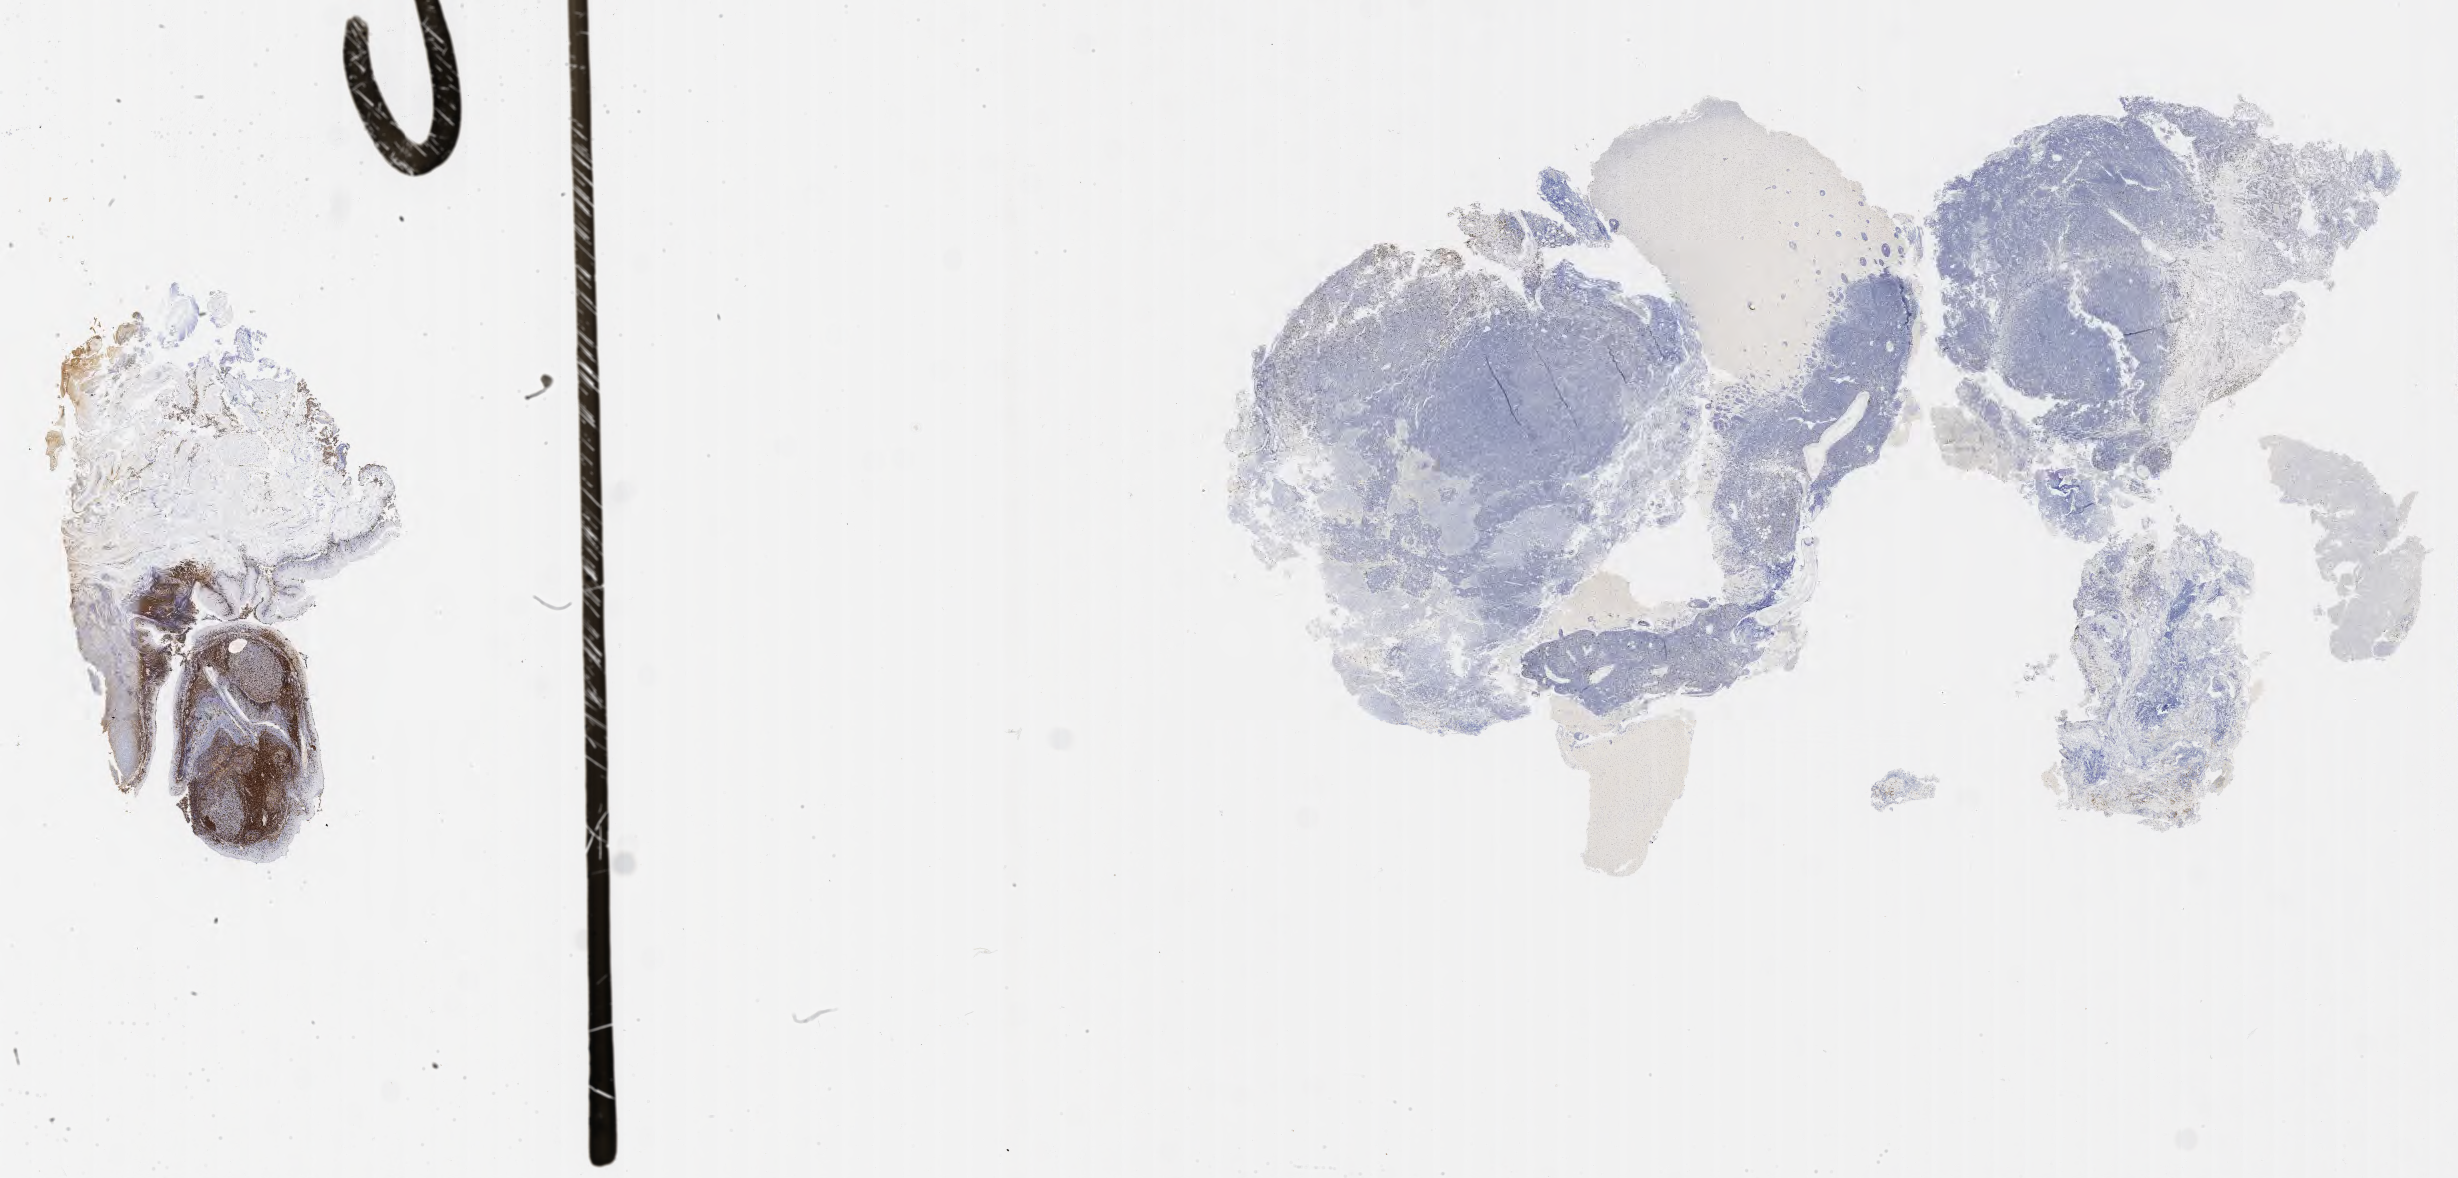
Immunohistochemistry (IHC) whole-slide image stained for CD3 — a low-resolution overview of the entire scanned area, about 39.8 x 19.1 mm, tumor tissue. Patient female; aged 73.
Histologic diagnosis: Burkitt lymphoma, NOS.